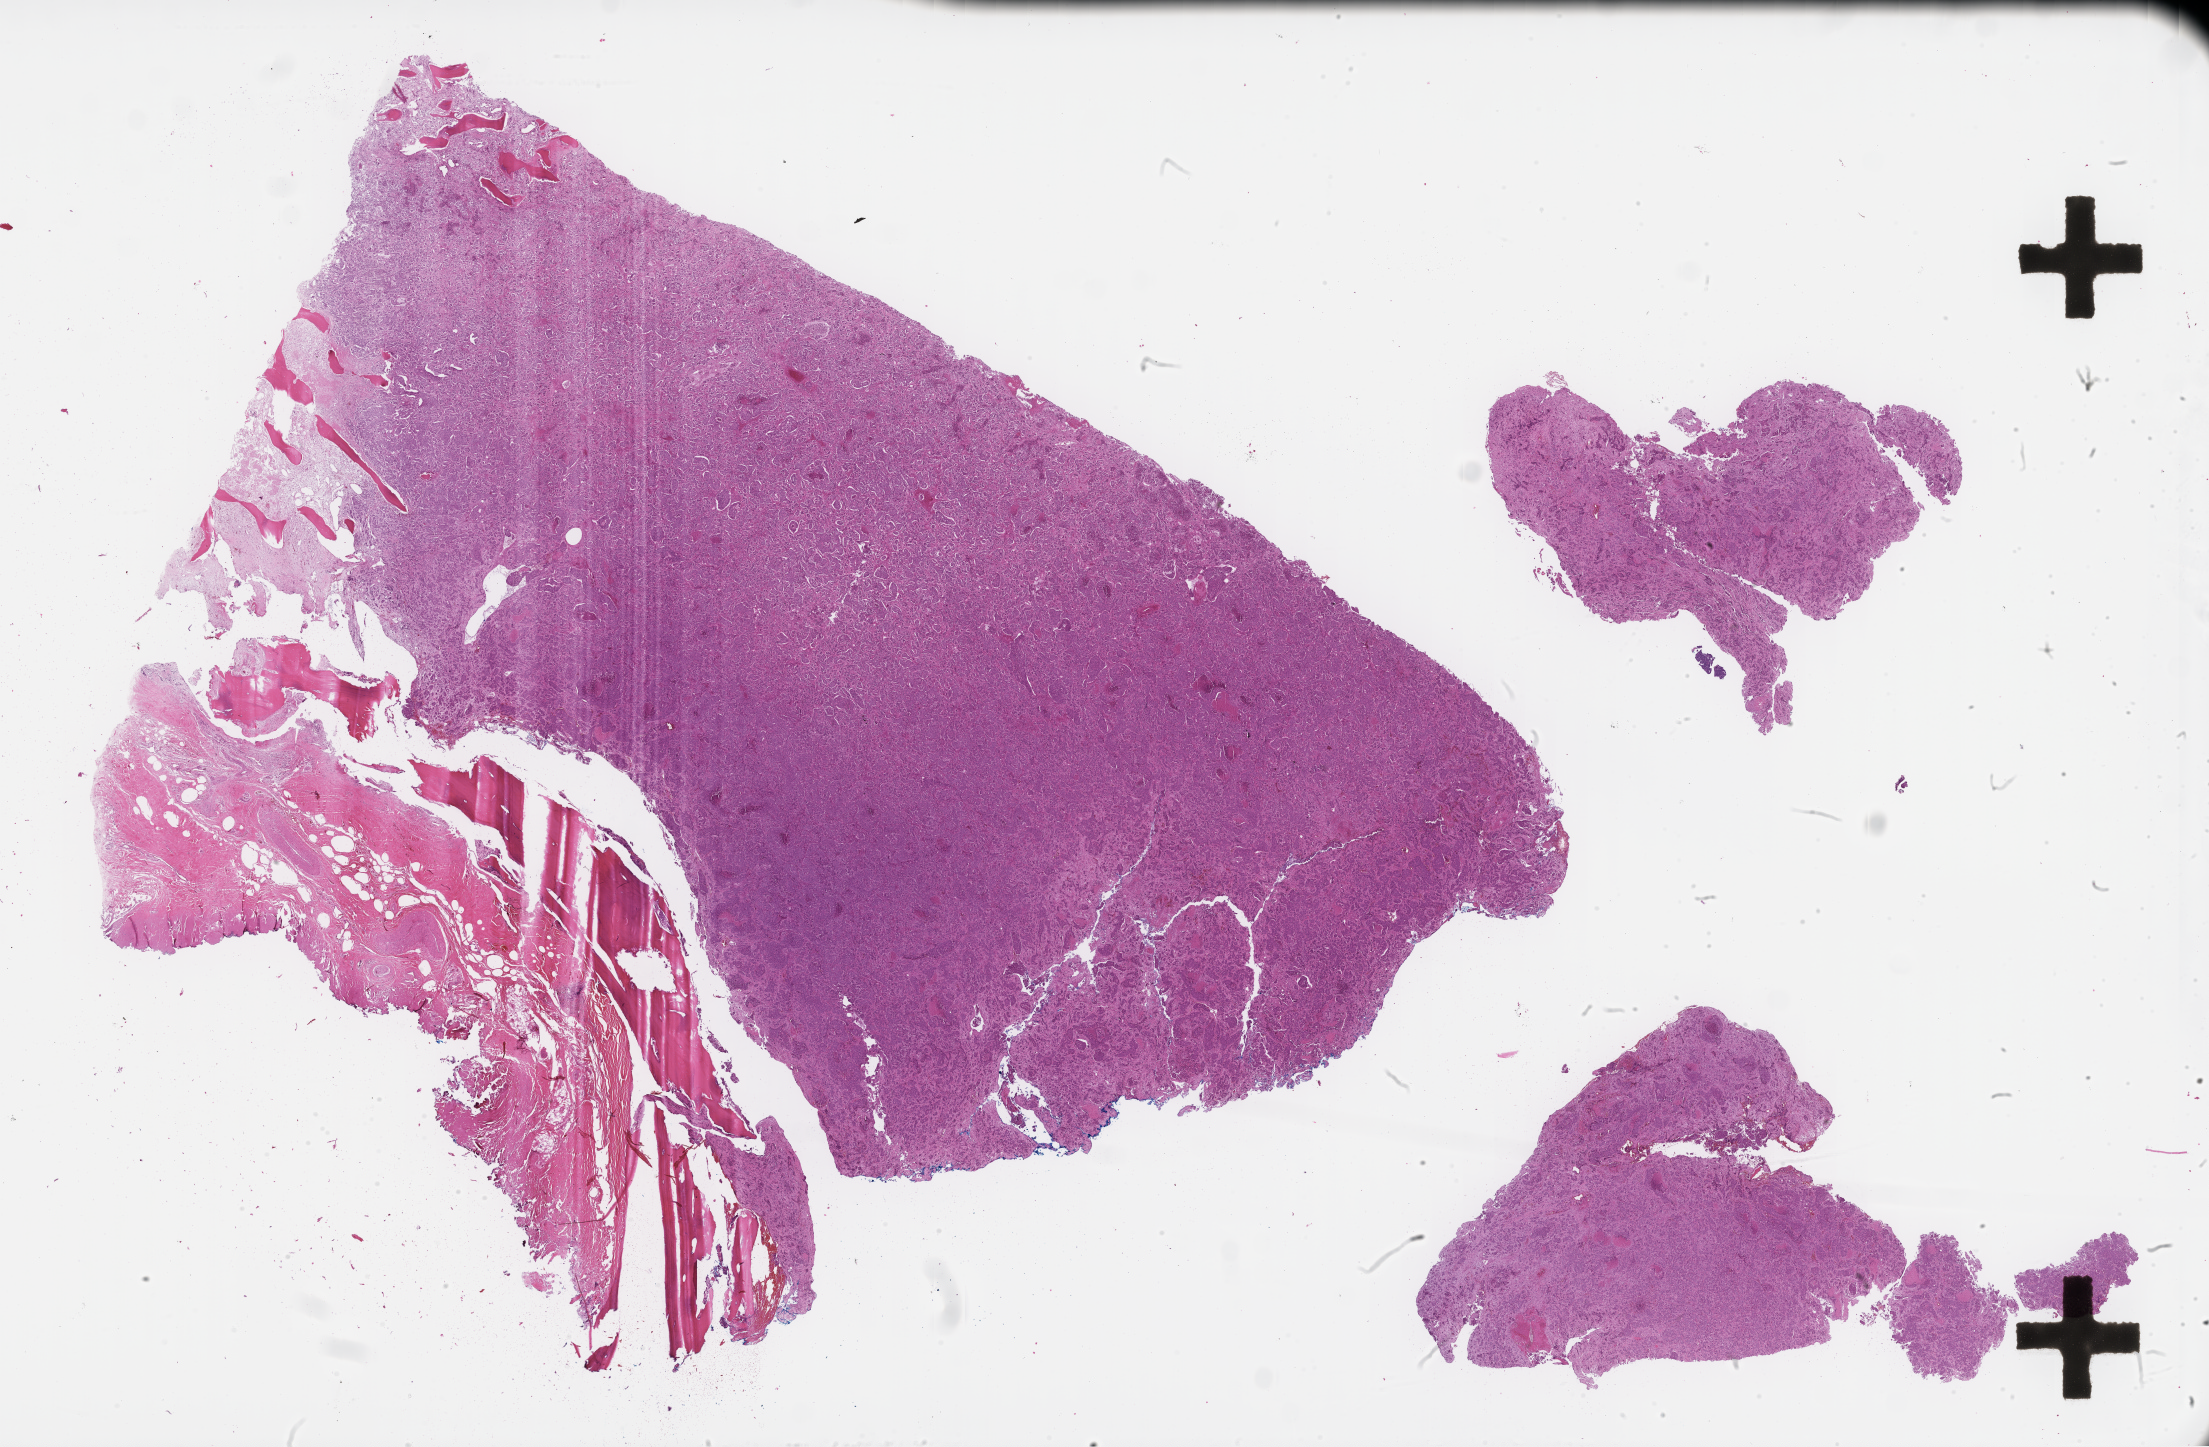
Haematoxylin and eosin whole-slide image — shown as a low-resolution overview of the whole scanned area (about 35.7 x 23.4 mm); formalin-fixed, paraffin-embedded (FFPE) tissue; archival tissue. Patient: female.
• this section: metastatic tumor tissue
• primary diagnosis of the patient: Invasive Breast Carcinoma